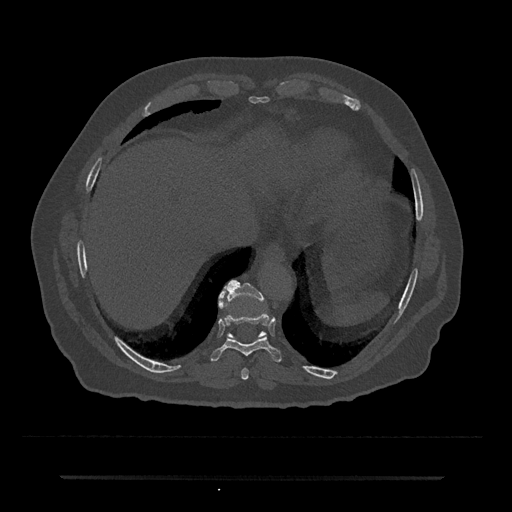
CT including the spine, one axial slice; slice 270 of 797 in the series (ordered by position); reconstruction kernel Br40s/3; 120 kVp; bone window (W 1800 / L 400 HU); 0.5 mm slice thickness; 512 × 512 image matrix. Male patient, age 69 years. Case-level facts recorded for this patient, not image findings: primary cancer: prostate.
Annotated regions visible in this slice (semi-automatic segmentation, software-assisted and operator-edited):
- T10 vertebra: bounding box <219,281,266,338> (left, top, right, bottom; pixels)
- T8 vertebra: <241,368,249,380>
- T9 vertebra: <210,290,282,362>